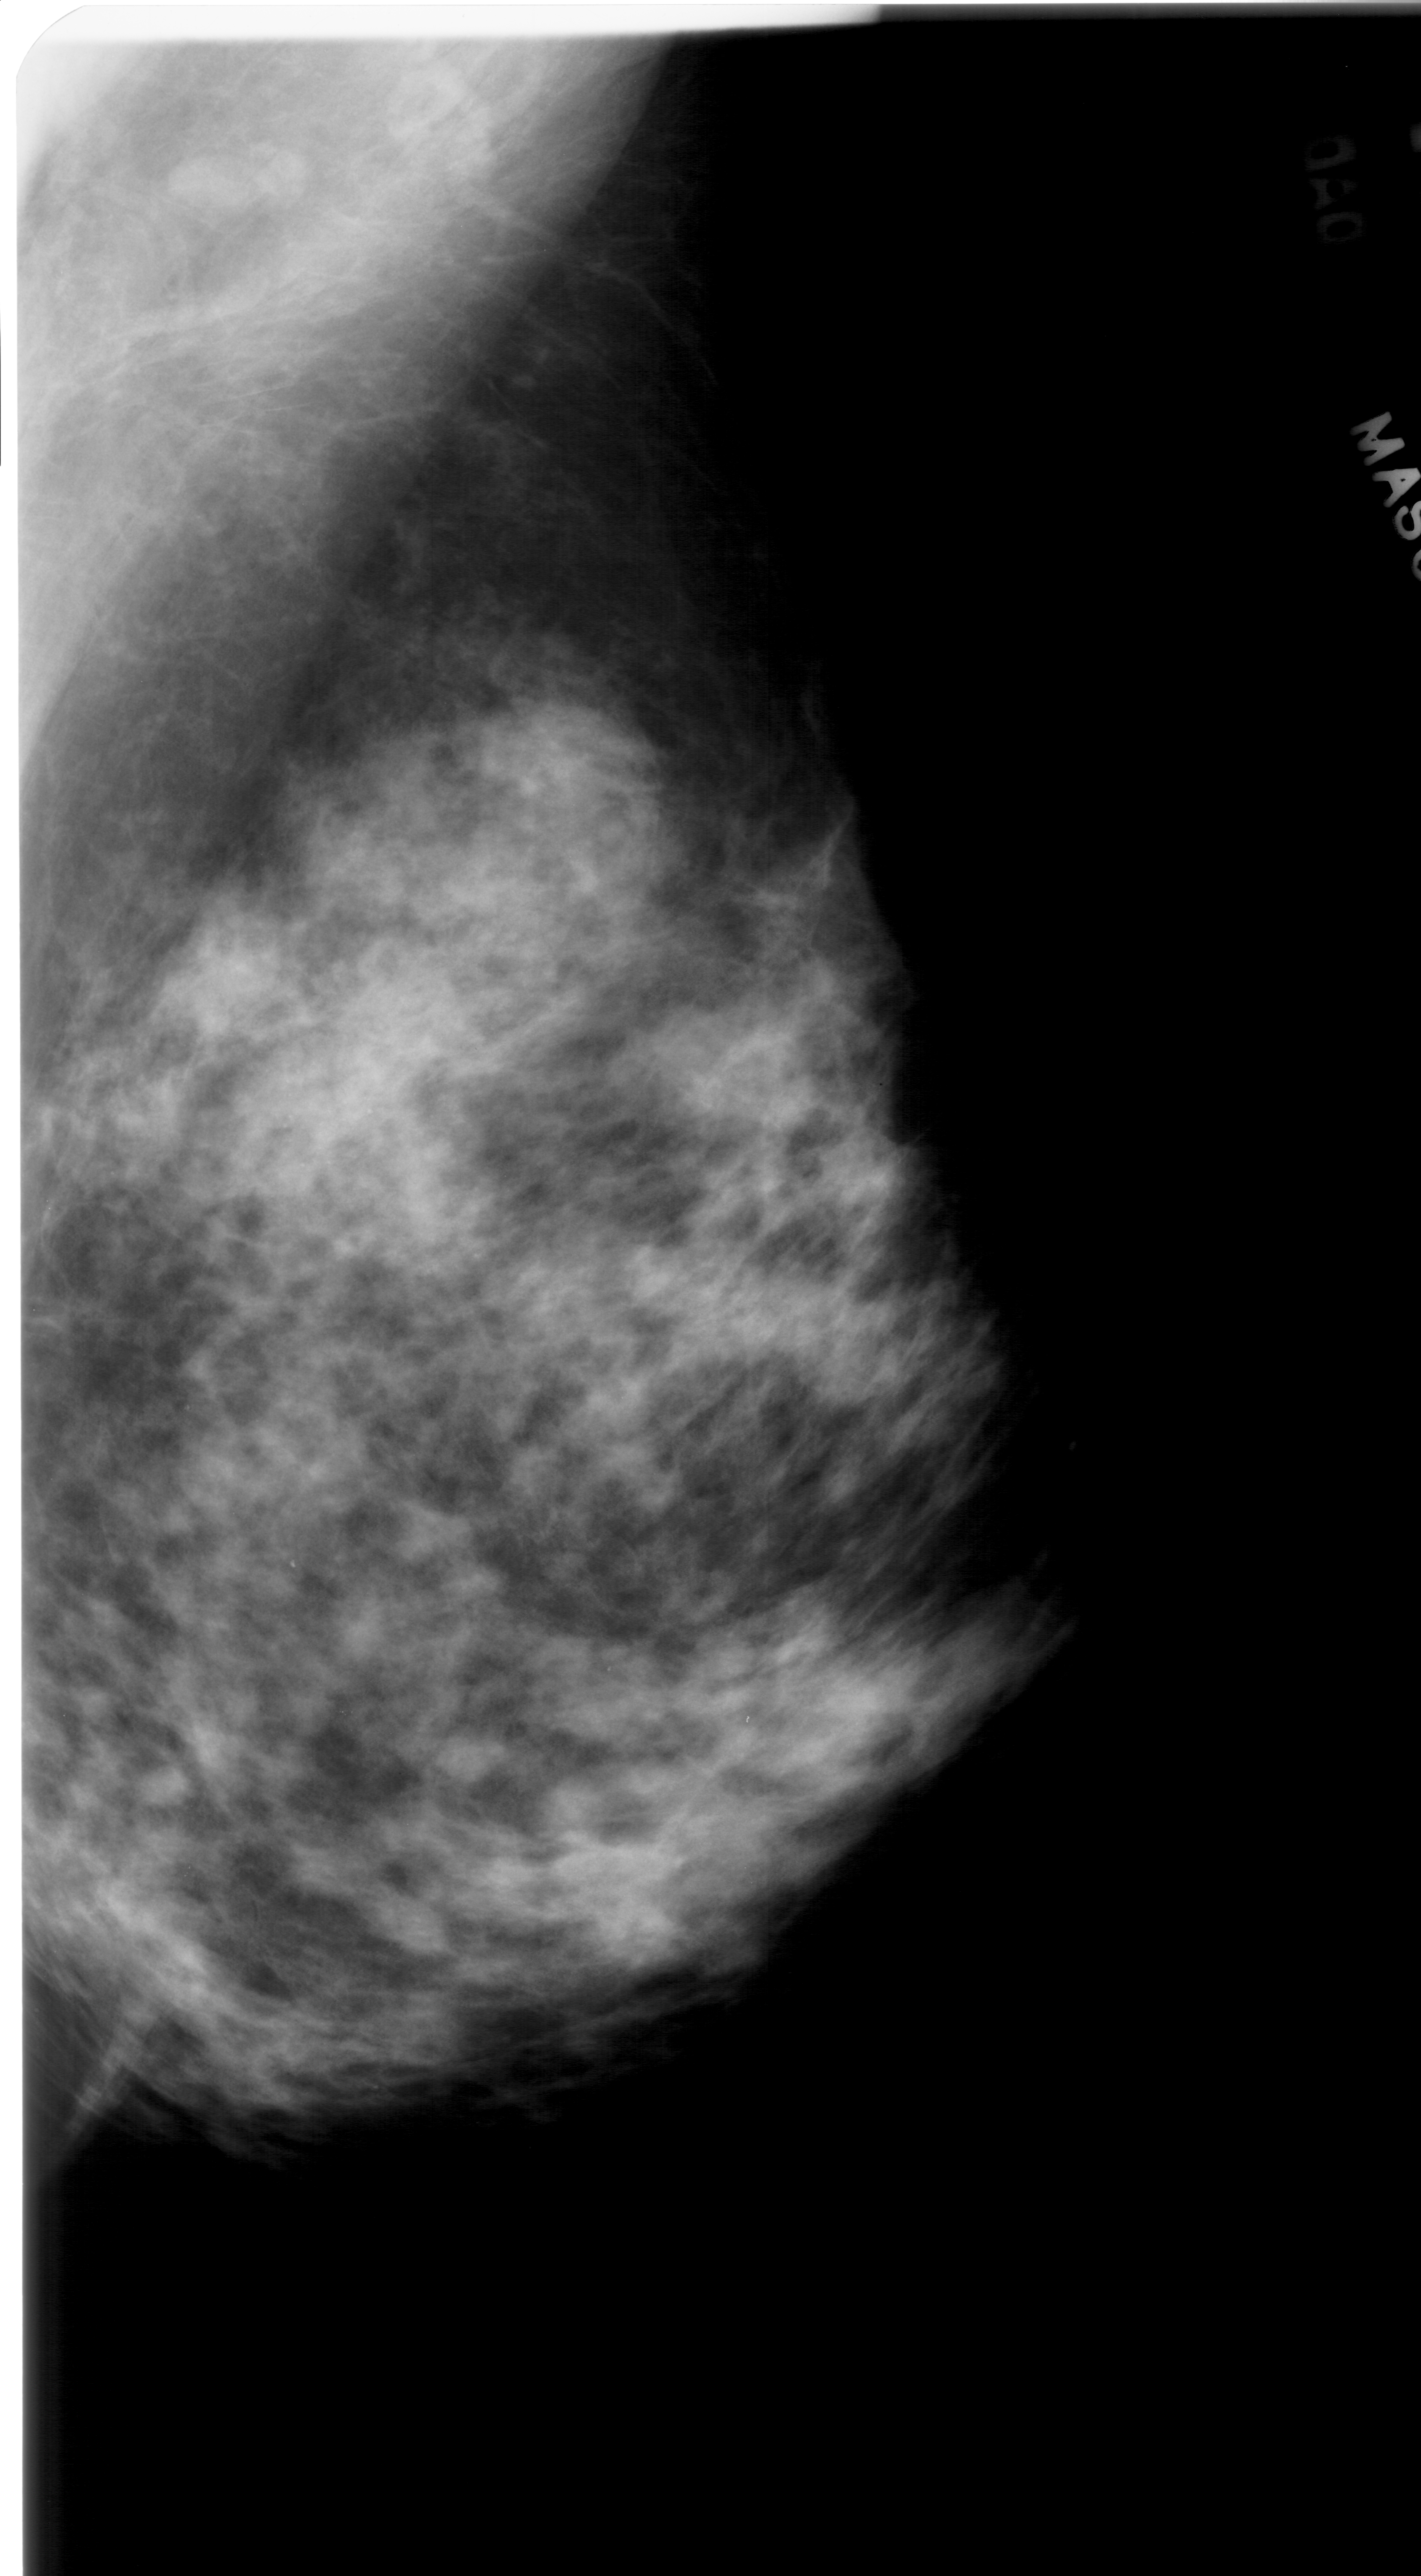
Scanned film-screen mammogram; right breast; MLO view; 1421 × 2576 image matrix.
Expert-marked regions of interest on this image (one box per marked abnormality):
- calcifications, morphology pleomorphic, distribution clustered; BI-RADS assessment category 4; pathology result (as recorded, not read from the image): benign: bounding box <277,1042,413,1184> (left, top, right, bottom; pixels)